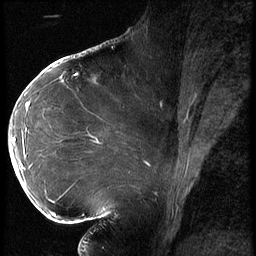
Breast MRI (dynamic contrast-enhanced), one sagittal slice; position 34 of 62 along the scan axis; 3 images stored at this slice position (order not interpretable as contrast timing); 1.5 T; TE 4.2 ms, TR 9 ms; 2.5 mm slice thickness; 256 × 256 image matrix, field of view 180 × 180 mm. Patient: female, 43 years. From the clinical record (not read from this slice): setting: breast cancer imaged before/during neoadjuvant chemotherapy; receptor status: HER2-positive.
Annotated regions visible in this slice (semi-automatic segmentation, software-assisted and operator-edited):
- analysis volume of interest (the breast-tissue region the enhancement analysis was run in; not a lesion): bounding box (x1, y1, x2, y2) in pixels: (9, 90, 82, 203)
- tumour enhancement mask (voxels above the 140 % enhancement threshold inside the analysis volume of interest): (12, 102, 29, 181)